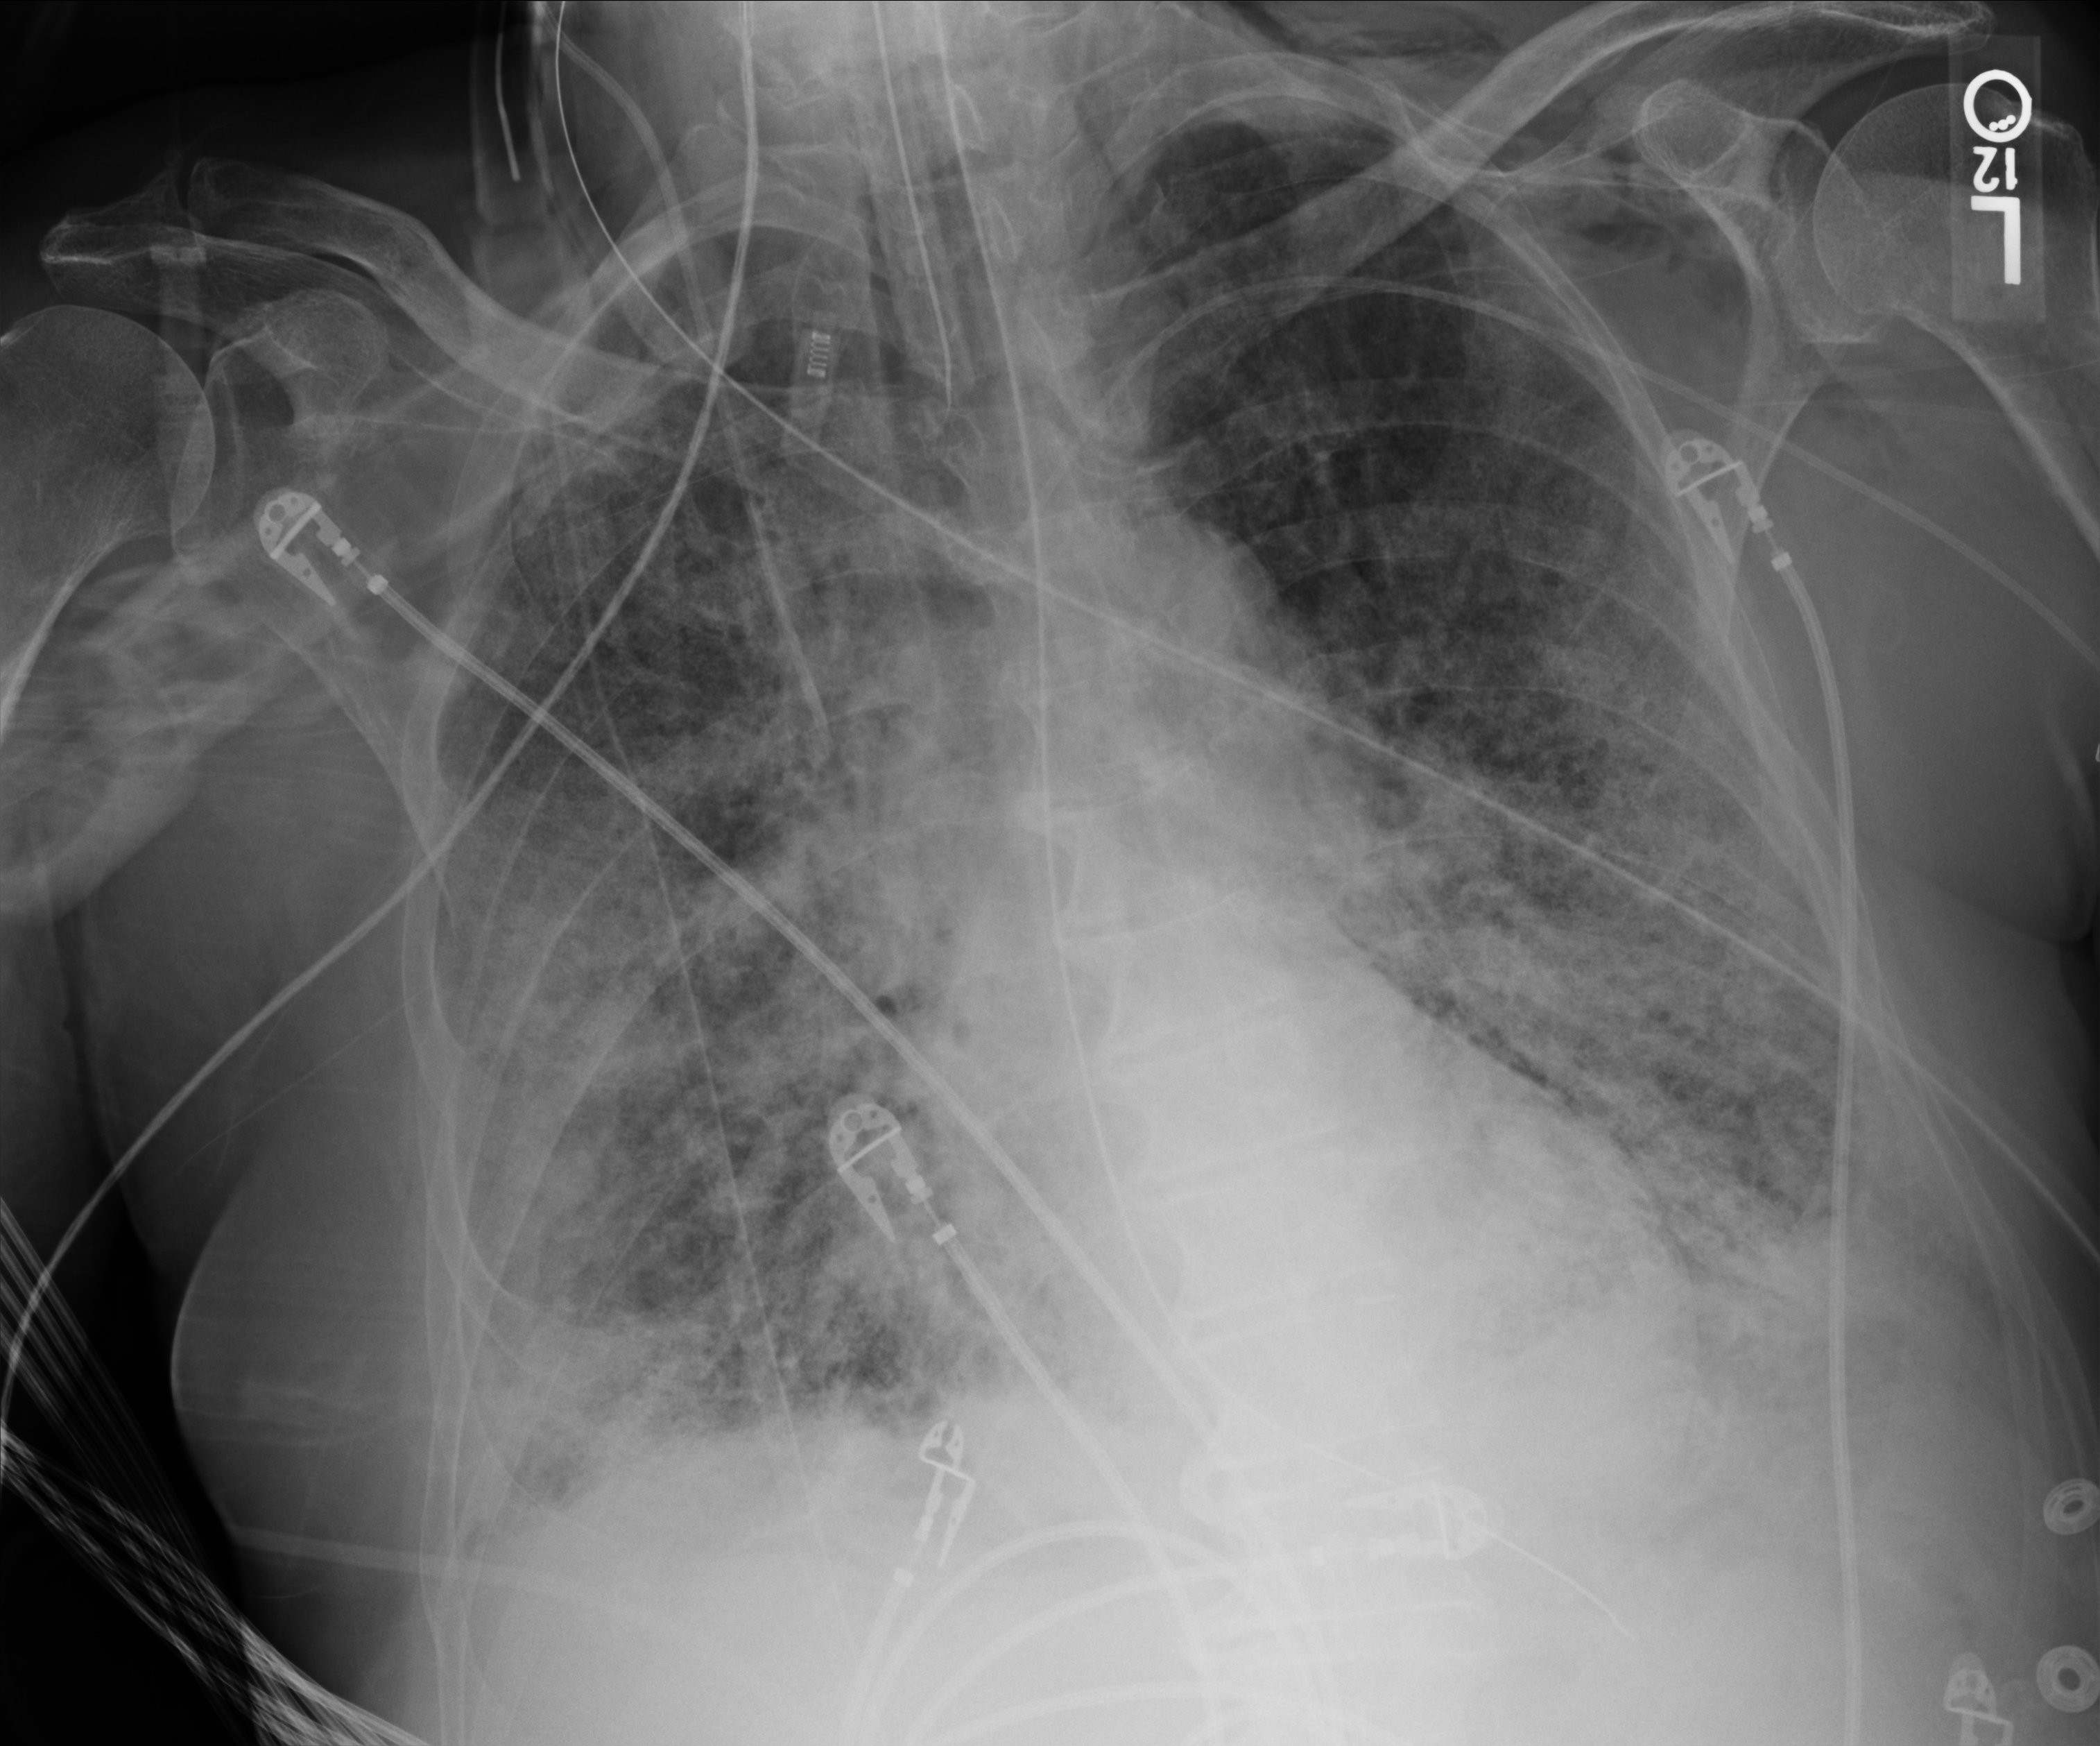
Bedside chest radiograph (computed radiography); anteroposterior (AP) projection. Patient hospitalised with COVID-19; male, aged 75–90 years.
Admission-level facts for this patient (not findings on this image; timing relative to this image not recorded): smoking status (admission record): never; chronic kidney disease (admission record): no.